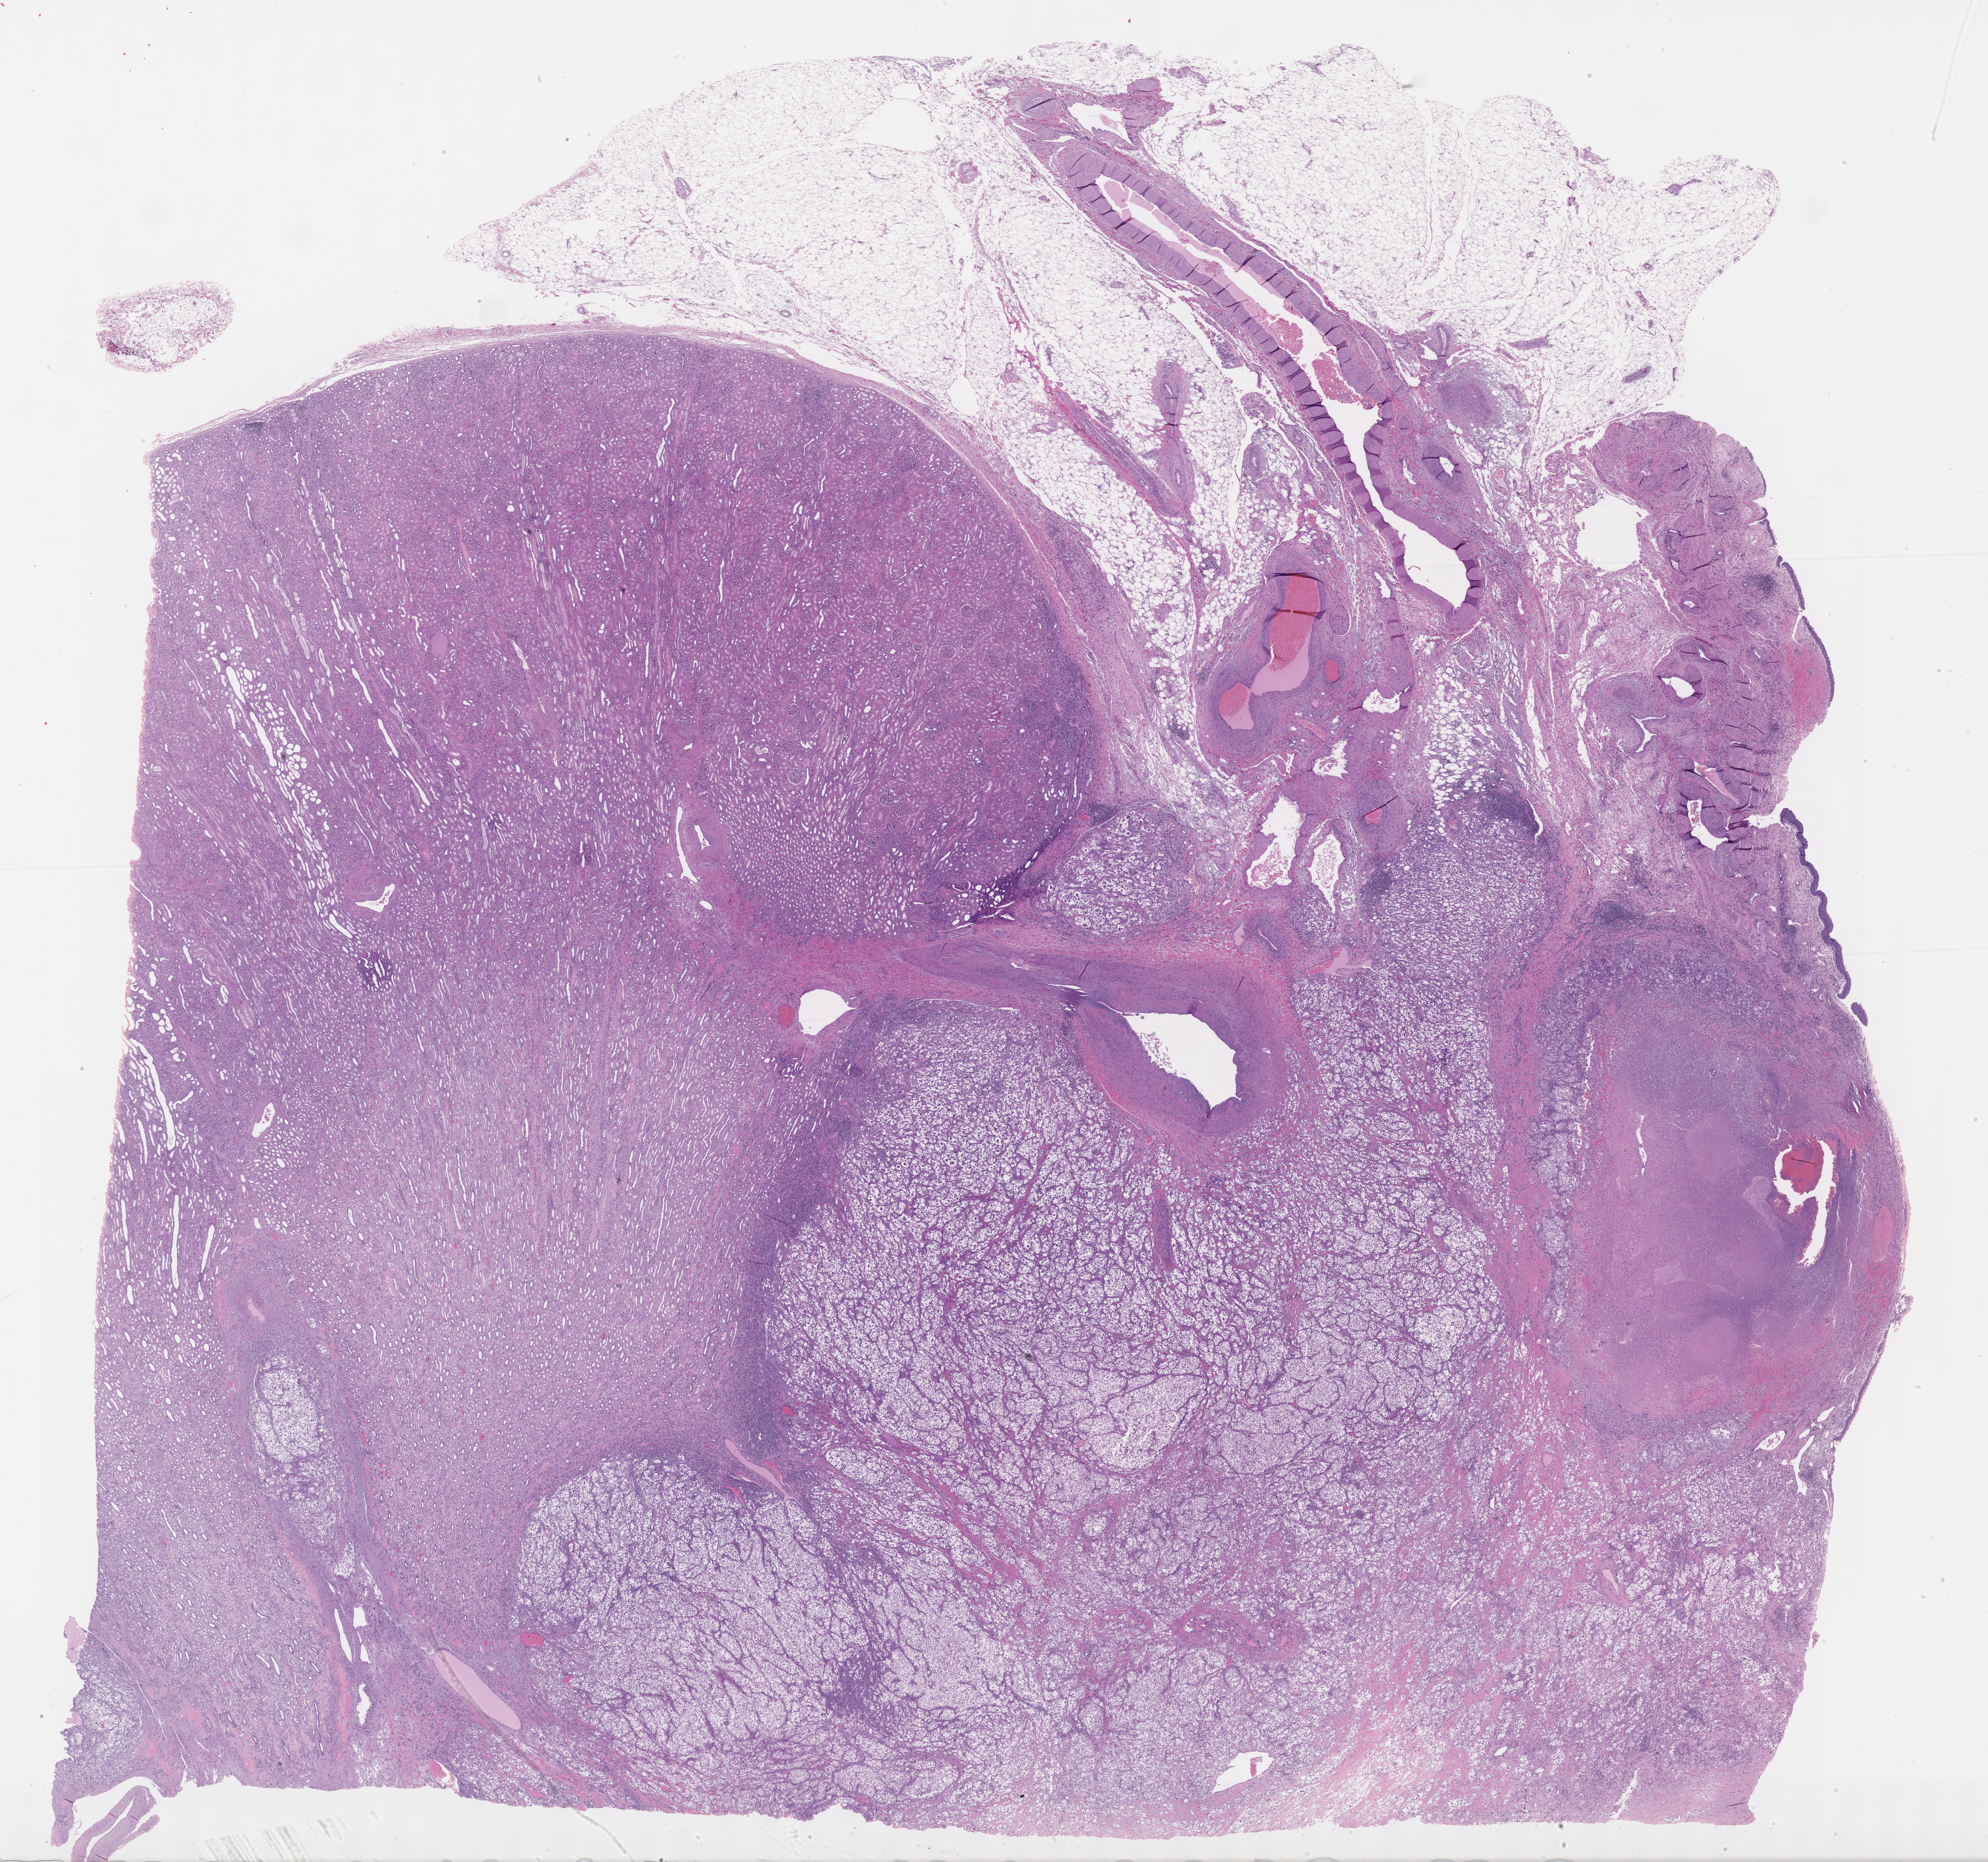
Hematoxylin and eosin (H&E) stained whole-slide image — low-resolution overview of the scanned area, about 24.2 x 22.6 mm. Formalin-fixed paraffin-embedded (FFPE) diagnostic section. Sample: primary tumour, kidney. Female patient; age at initial diagnosis 63 years. Histologic grade: G4 (undifferentiated).
AJCC pathologic stage: IV. Diagnosis: Clear cell adenocarcinoma, NOS. Laterality: left.